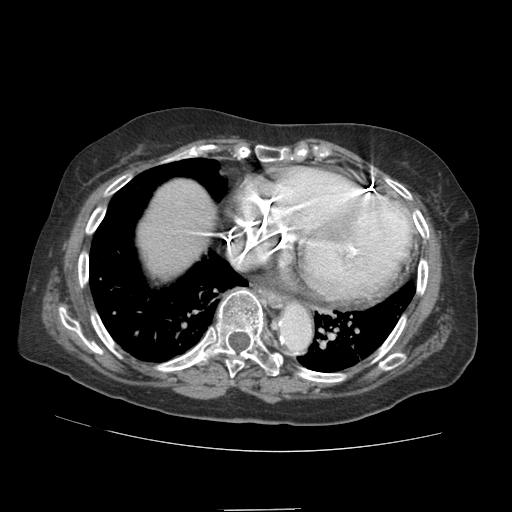
Contrast-enhanced abdominal CT (liver protocol), one axial slice; position 81 of 89 along the scan axis; 140 kVp; soft-tissue window (W 400 / L 40 HU); 2.5 mm slice thickness; 512 × 512 image matrix, field of view 360 × 360 mm. From the clinical record (not read from this slice): diagnosis: hepatocellular carcinoma (patient treated with transarterial chemoembolisation; whether this scan precedes or follows treatment is not stated here); TNM stage (as recorded): Stage-II; Child-Pugh class: A; tumour differentiation: moderately differentiated; tumour nodularity: multinodular.
Annotated regions visible in this slice (semi-automatic segmentation, software-assisted and operator-edited):
- abdominal aorta: bounding box [x1, y1, x2, y2] px = [280, 305, 310, 346]
- liver parenchyma outside the tumour (the mass and vessels are separate outlines, so this box may not span the whole liver): [138, 178, 216, 276]
- liver vessels: [196, 232, 211, 236]